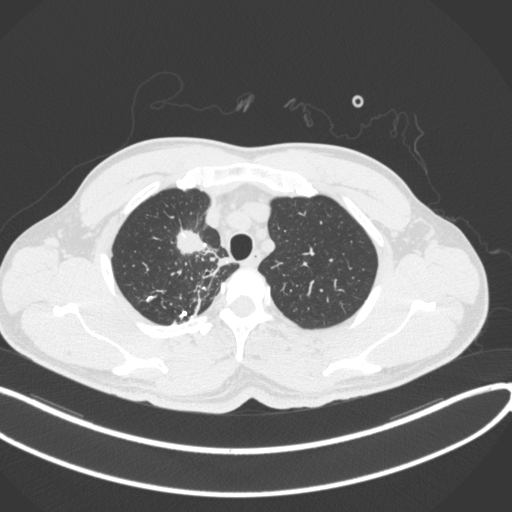
Chest CT, one axial slice. Position 312 of 391 along the scan axis. 120 kVp. Lung window (W 1500 / L -600 HU). 1 mm slice thickness. 512 × 512 image matrix, field of view 400 × 400 mm. Male patient, age 48 years. From the clinical record (not read from this slice): clinical TNM (as recorded): T1c N1 M1.
Annotated regions visible in this slice (rectangle marked by the reading radiologist):
- lung tumour (recorded histology: adenocarcinoma): bounding box <170,220,214,260> (left, top, right, bottom; pixels)